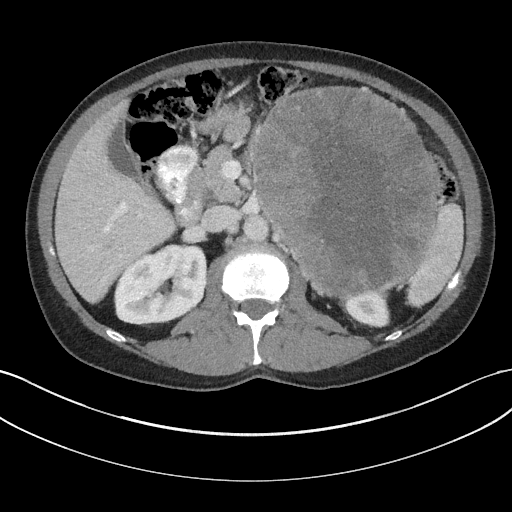
Contrast-enhanced abdominal CT, one axial slice; position 104 of 147 along the scan axis; 100 kVp; soft-tissue window (W 400 / L 40 HU); 512 × 512 image matrix, field of view 384 × 384 mm. Male patient, age 58 years. Case-level facts recorded for this patient, not image findings: diagnosis: adrenocortical carcinoma; tumour side: left adrenal; tumour size at pathology: 22 cm.
Annotated regions visible in this slice (semi-automatic segmentation, software-assisted and operator-edited):
- mass: bounding box <256,87,435,296> (left, top, right, bottom; pixels)